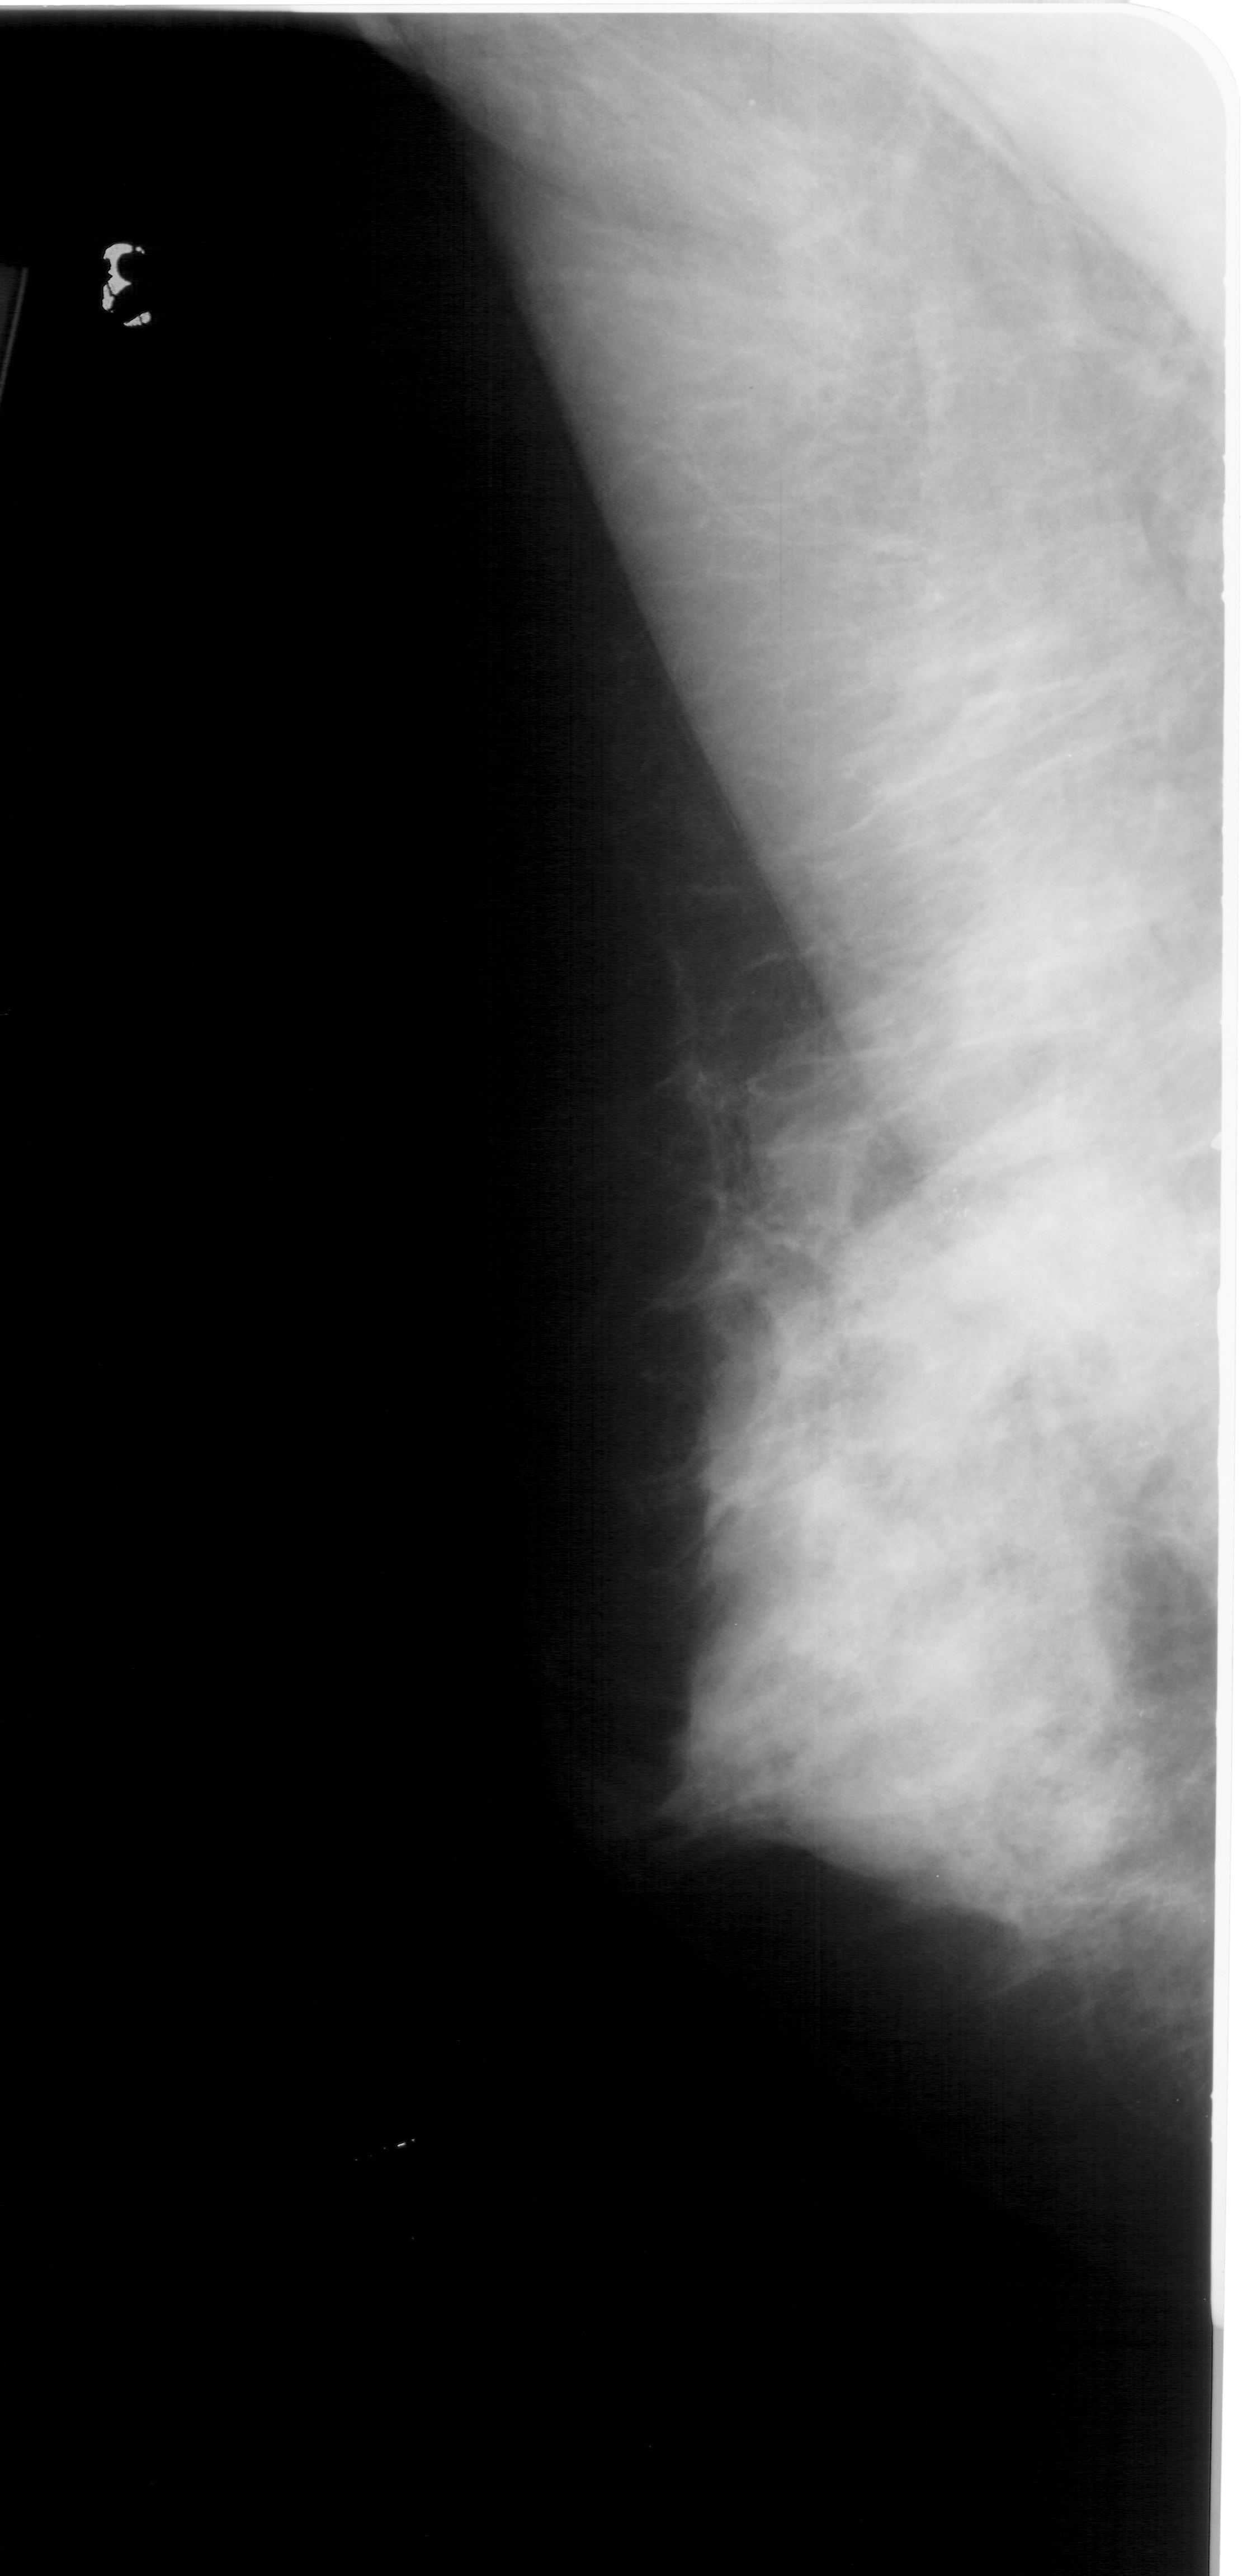
Digitized screen-film mammogram; left breast; MLO view; BI-RADS breast density category 4 (scale 1–4); 1242 × 2576 image matrix.
Expert-marked regions of interest on this image (one box per marked abnormality):
- calcifications, morphology pleomorphic, distribution clustered; BI-RADS assessment category 4; subtlety rating 2 on a 1 (subtle) to 5 (obvious) scale; pathology (as recorded): malignant: box from (x=923, y=1187) to (x=996, y=1243) px